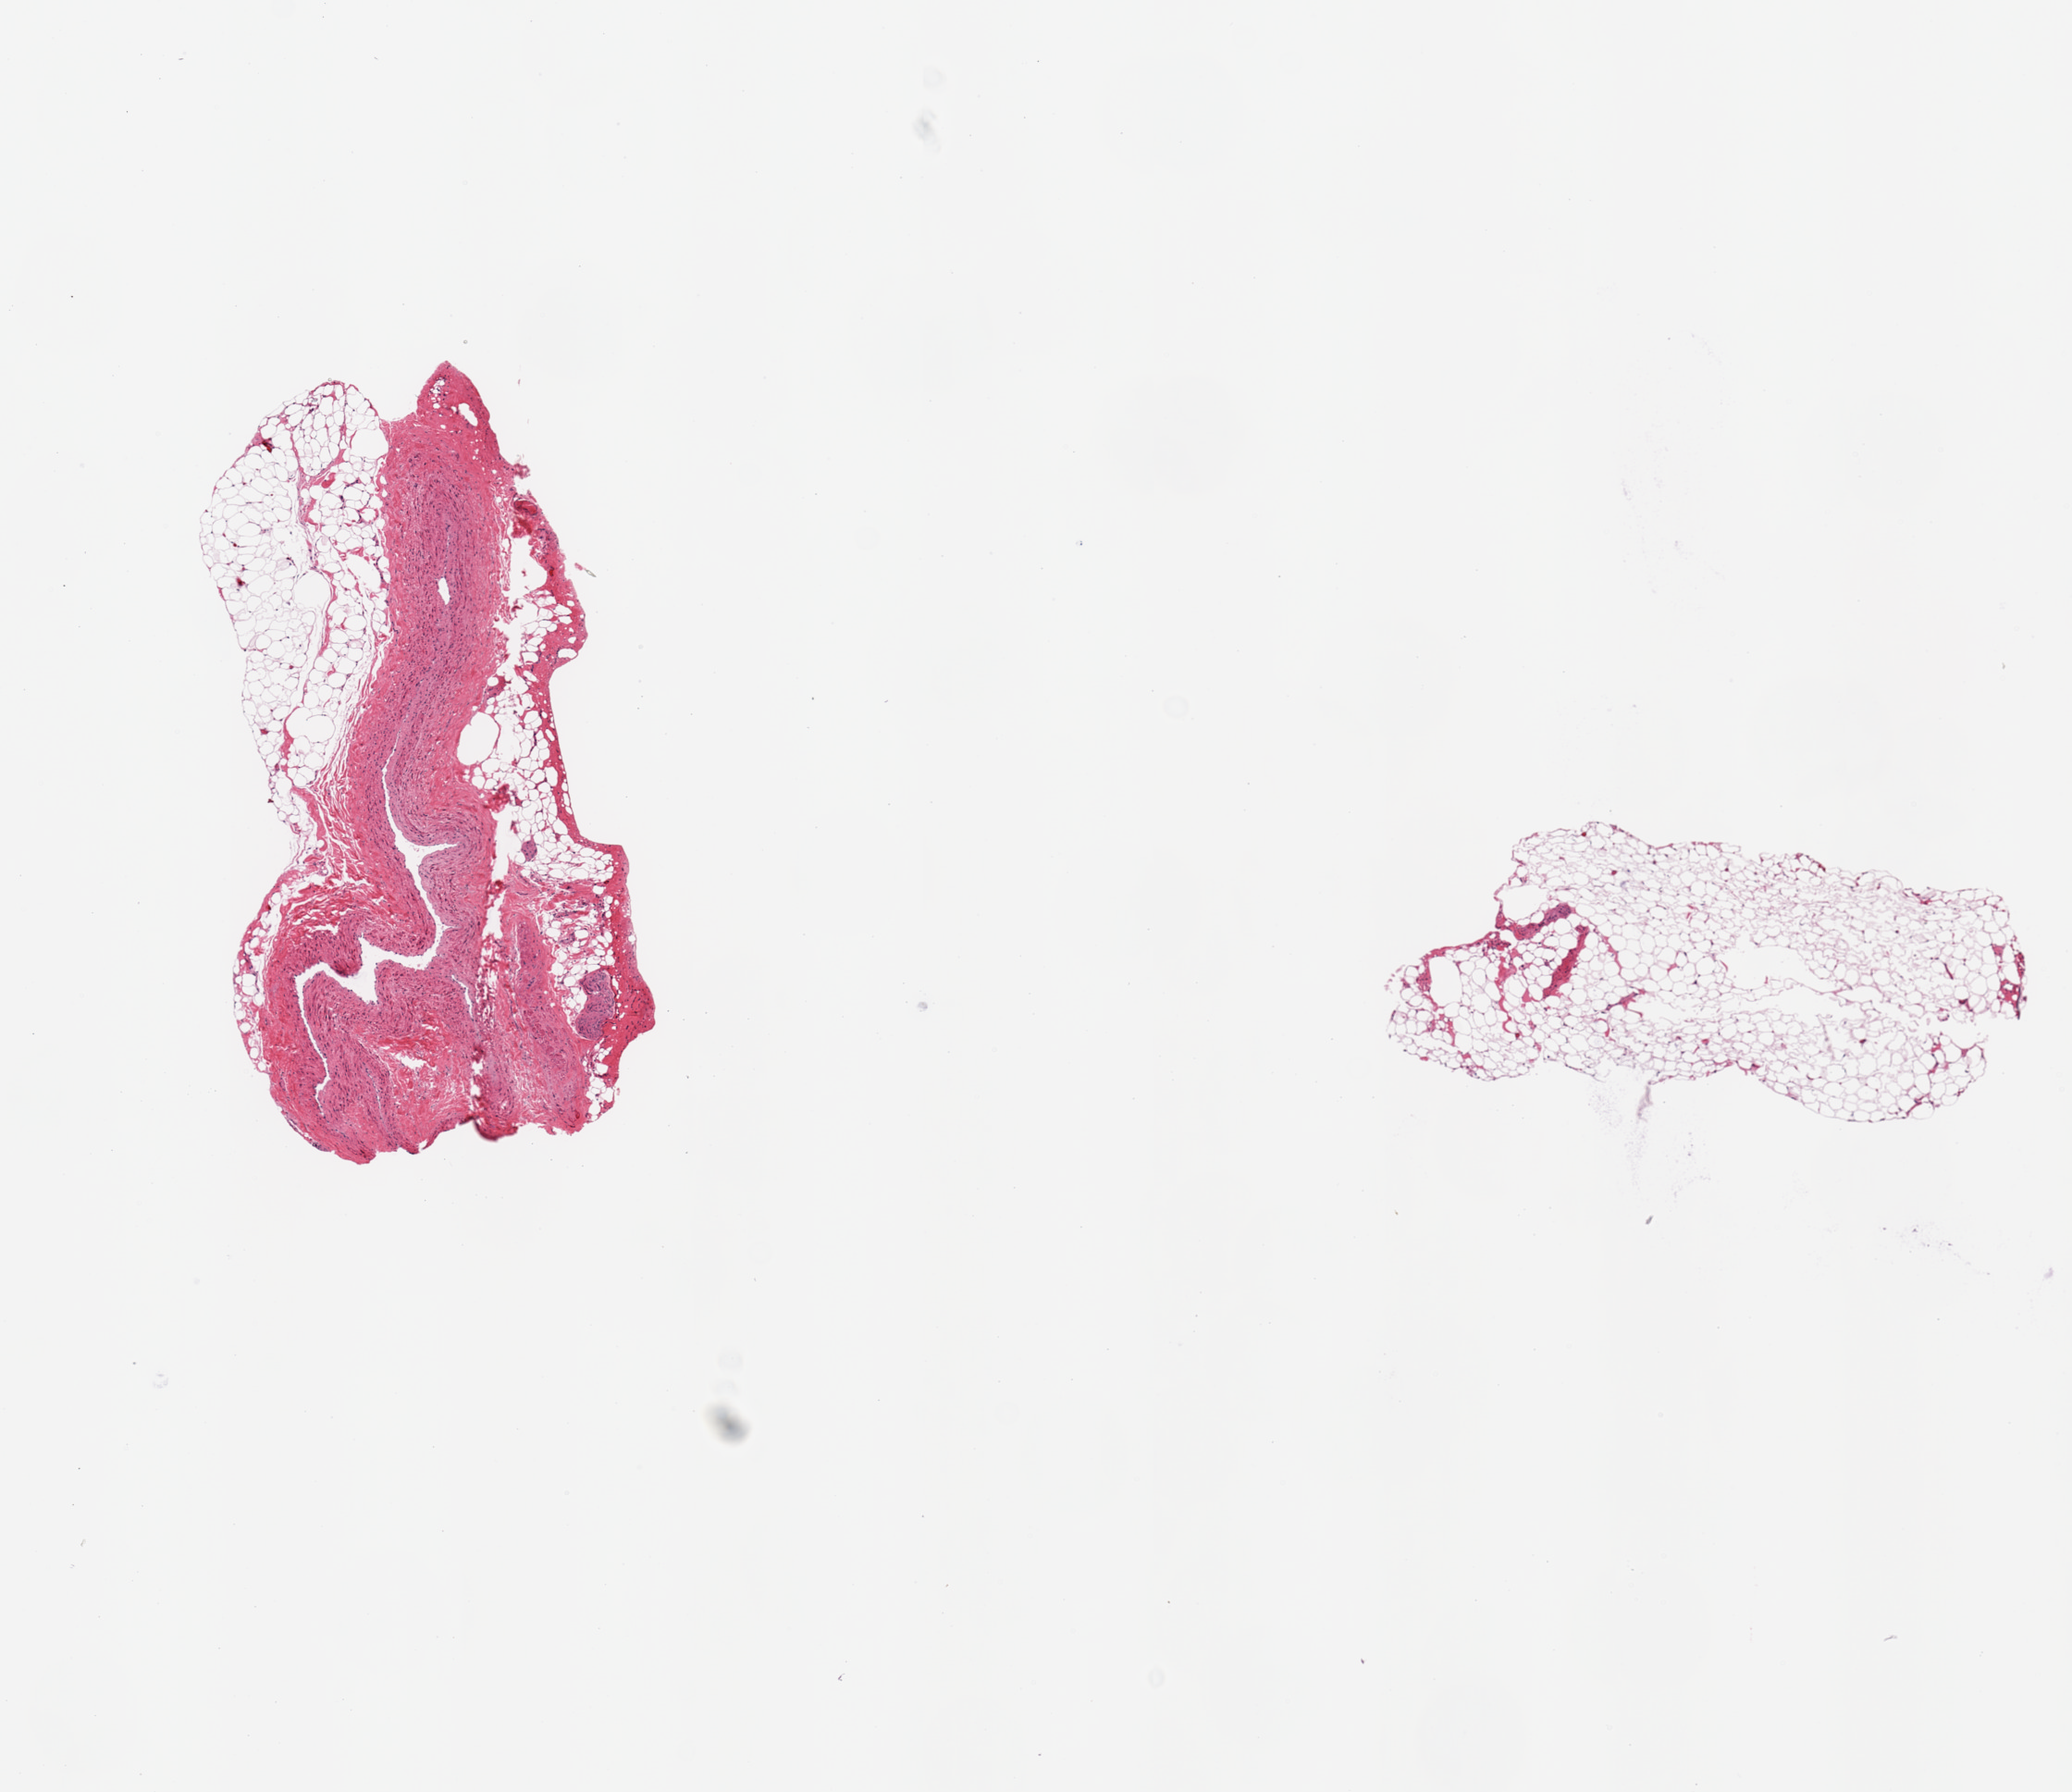
Whole-slide image, haematoxylin and eosin stain, low-resolution overview of the scanned area, about 8.9 x 7.7 mm (slide scanned at 20x); PAXgene-fixed paraffin-embedded (PFPE) section; target tissue: coronary artery; tissue donor sample. Donor sex: male.
Review note (as recorded): 2 pieces,~3.3x1.6mm vein w/30% fat; other piece is only fat.